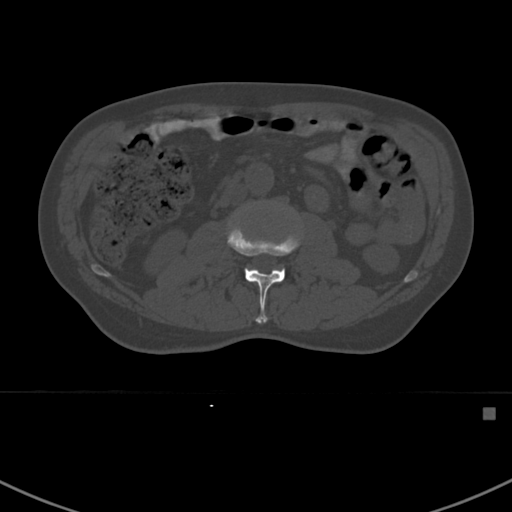
CT including the spine, one axial slice. Slice 281 of 412 in the series (ordered by position). Reconstruction kernel Br40s. Bone window (W 1800 / L 400 HU). 1.5 mm slice thickness. 512 × 512 image matrix, field of view 358 × 358 mm. Male patient, age 59 years. Case-level facts recorded for this patient, not image findings: primary cancer: prostate.
Outlined on this slice (semi-automatically segmented with operator editing):
- L2 vertebra: bounding box [x1, y1, x2, y2] px = [227, 222, 301, 323]